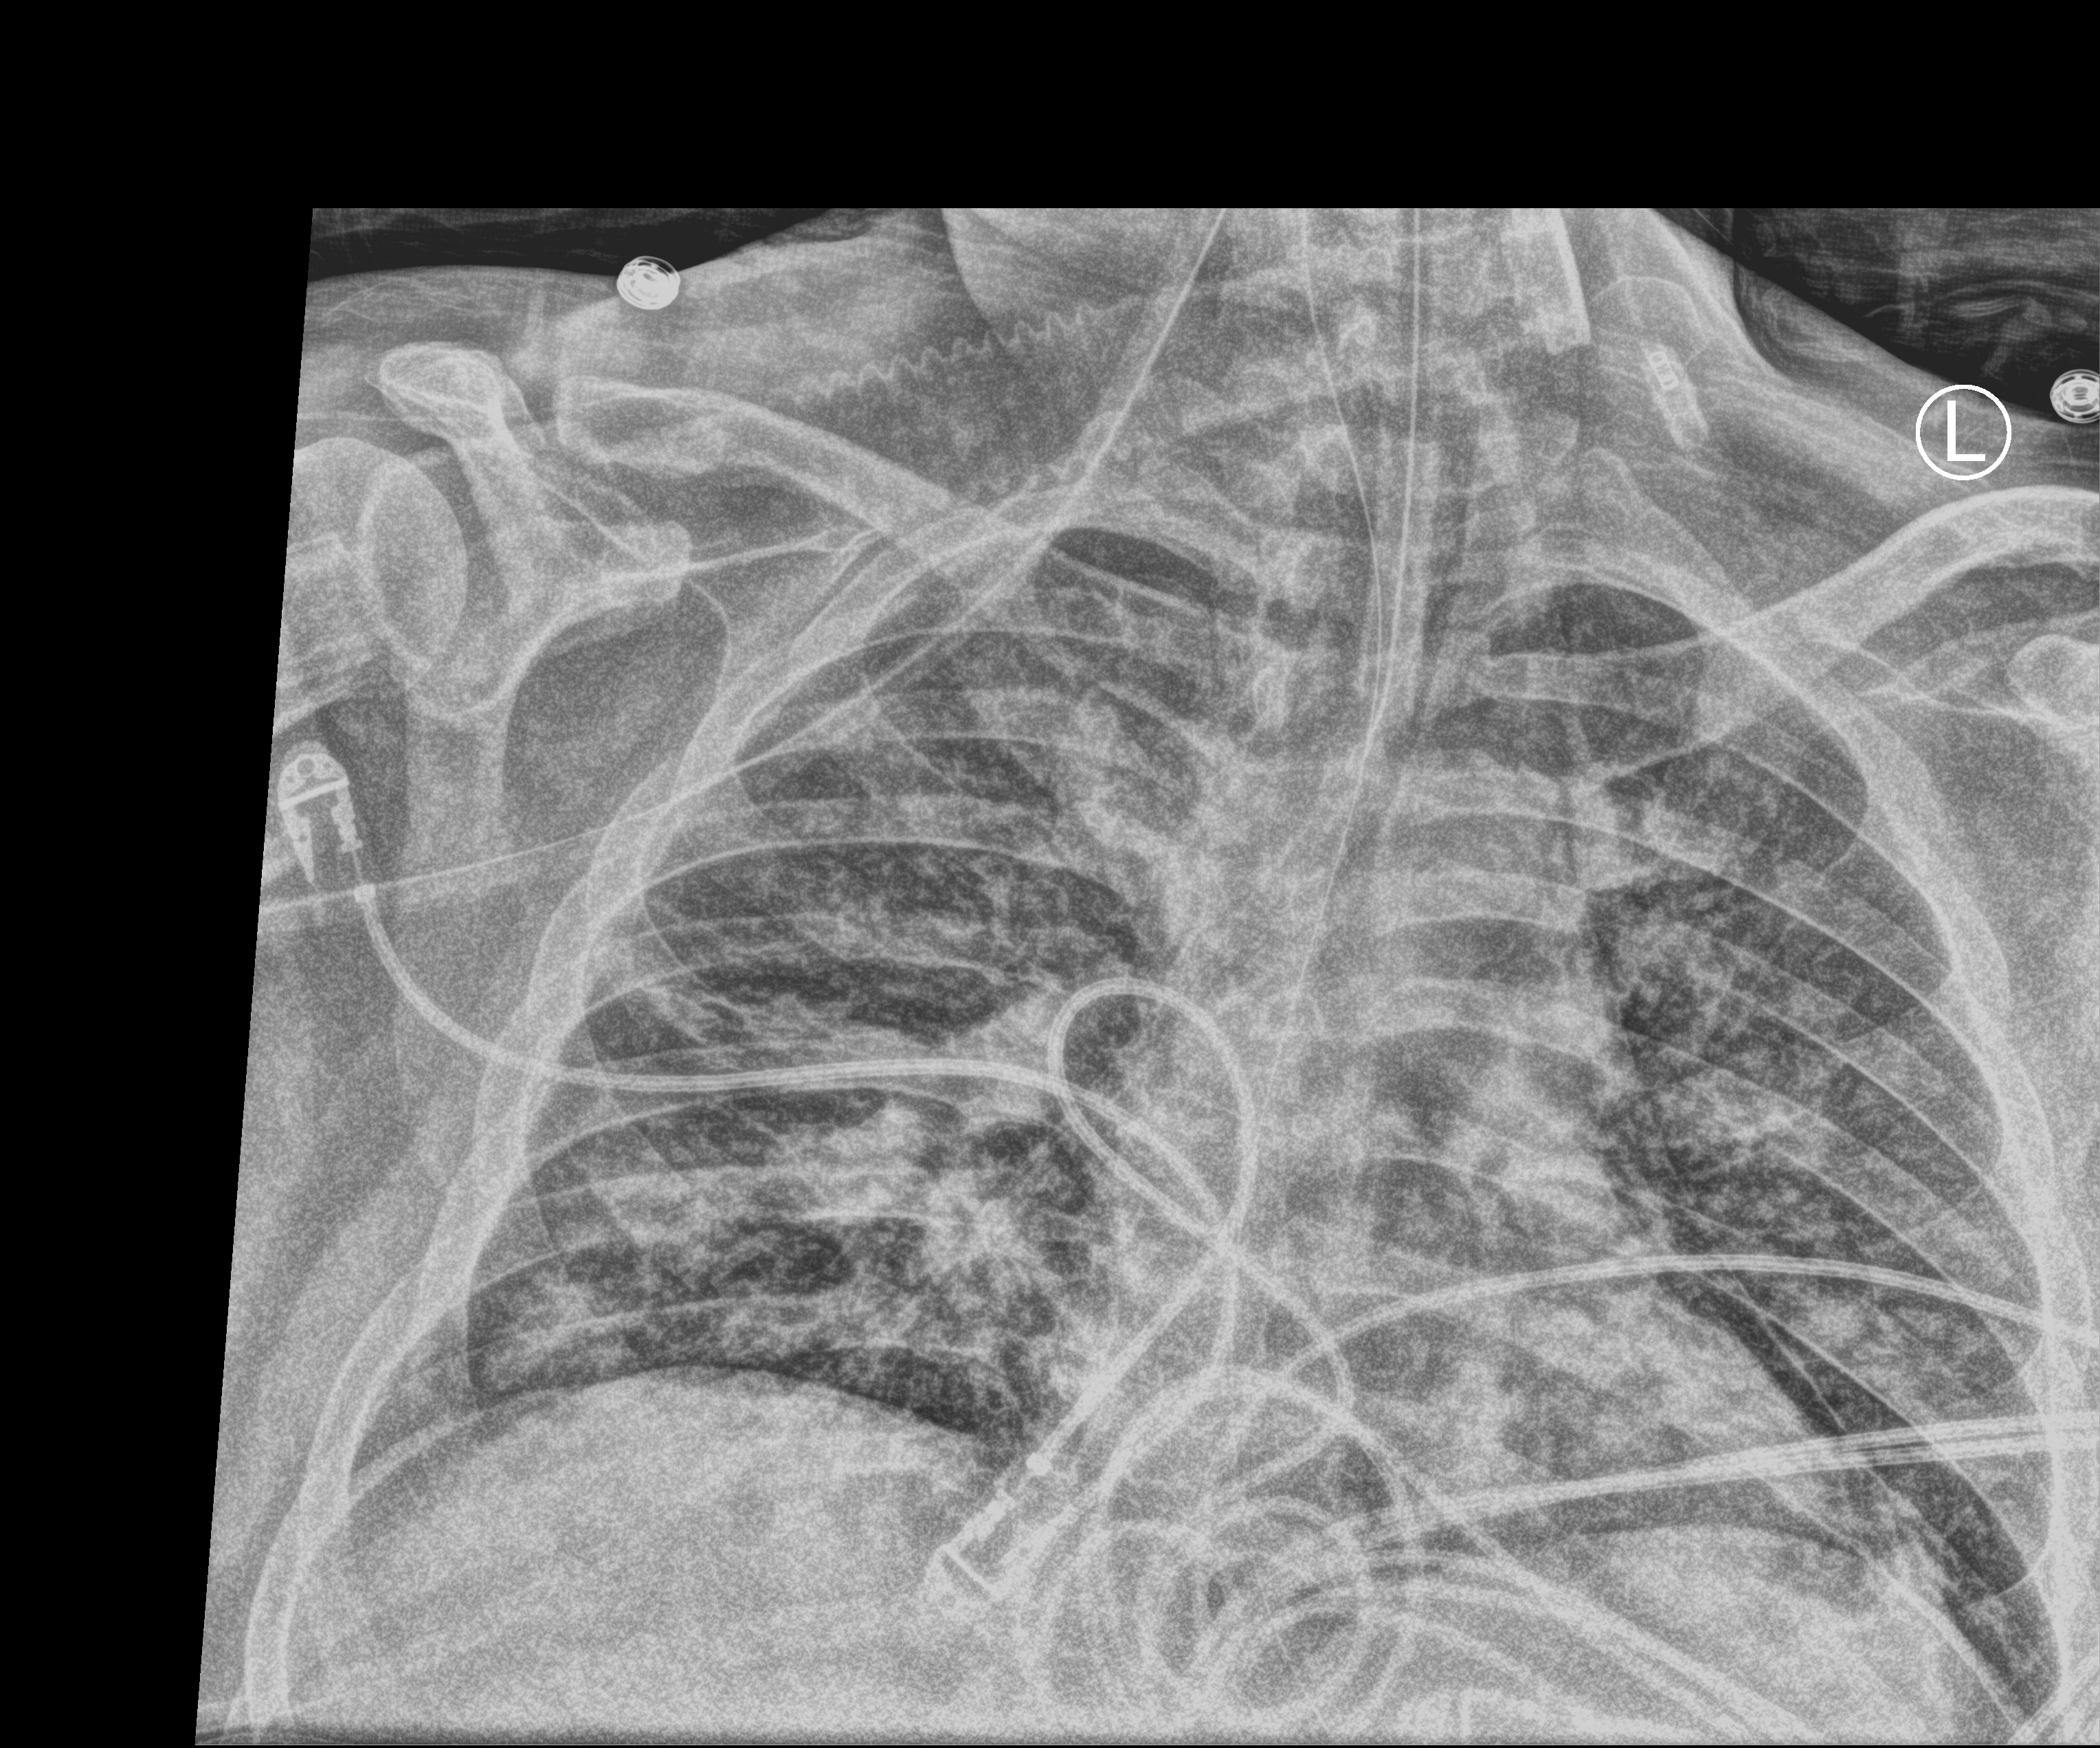
Chest X-ray (portable), anteroposterior (AP) projection. Patient hospitalised with COVID-19, aged 18–59 years.
Hospital-stay facts (about this admission, not read from this image; timing relative to this image not recorded):
- mechanically ventilated during this hospital stay: yes
- admitted to intensive care during this hospital stay: yes
- length of hospital stay: 31 days